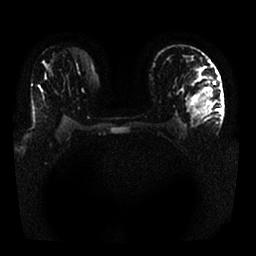
Breast MRI, one axial slice. Position 18 of 25 along the scan axis. Diffusion-weighted series; image 2 of 4 stored at this slice position (different b-values; order by instance number). 1.5 T. 4 mm slice thickness. 256 × 256 image matrix, field of view 340 × 340 mm. Female patient.
Structures marked on this image (expert manual segmentation):
- tumour on diffusion-weighted imaging: bounding box [x1, y1, x2, y2] px = [198, 104, 209, 113]